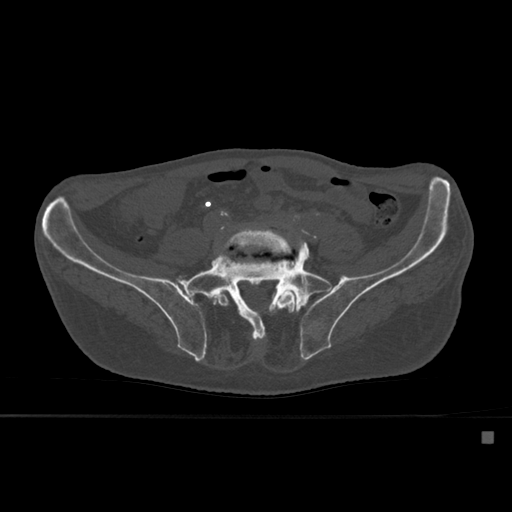
CT including the spine, one axial slice. Position 166 of 527 along the scan axis. Bone window (W 1800 / L 400 HU). 1.5 mm slice thickness. 512 × 512 image matrix, field of view 373 × 373 mm. Patient: male, 78 years. From the clinical record (not read from this slice): primary cancer: prostate.
Structures marked on this image (semi-automatically segmented with operator editing):
- L5 vertebra: box from (x=211, y=227) to (x=297, y=313) px